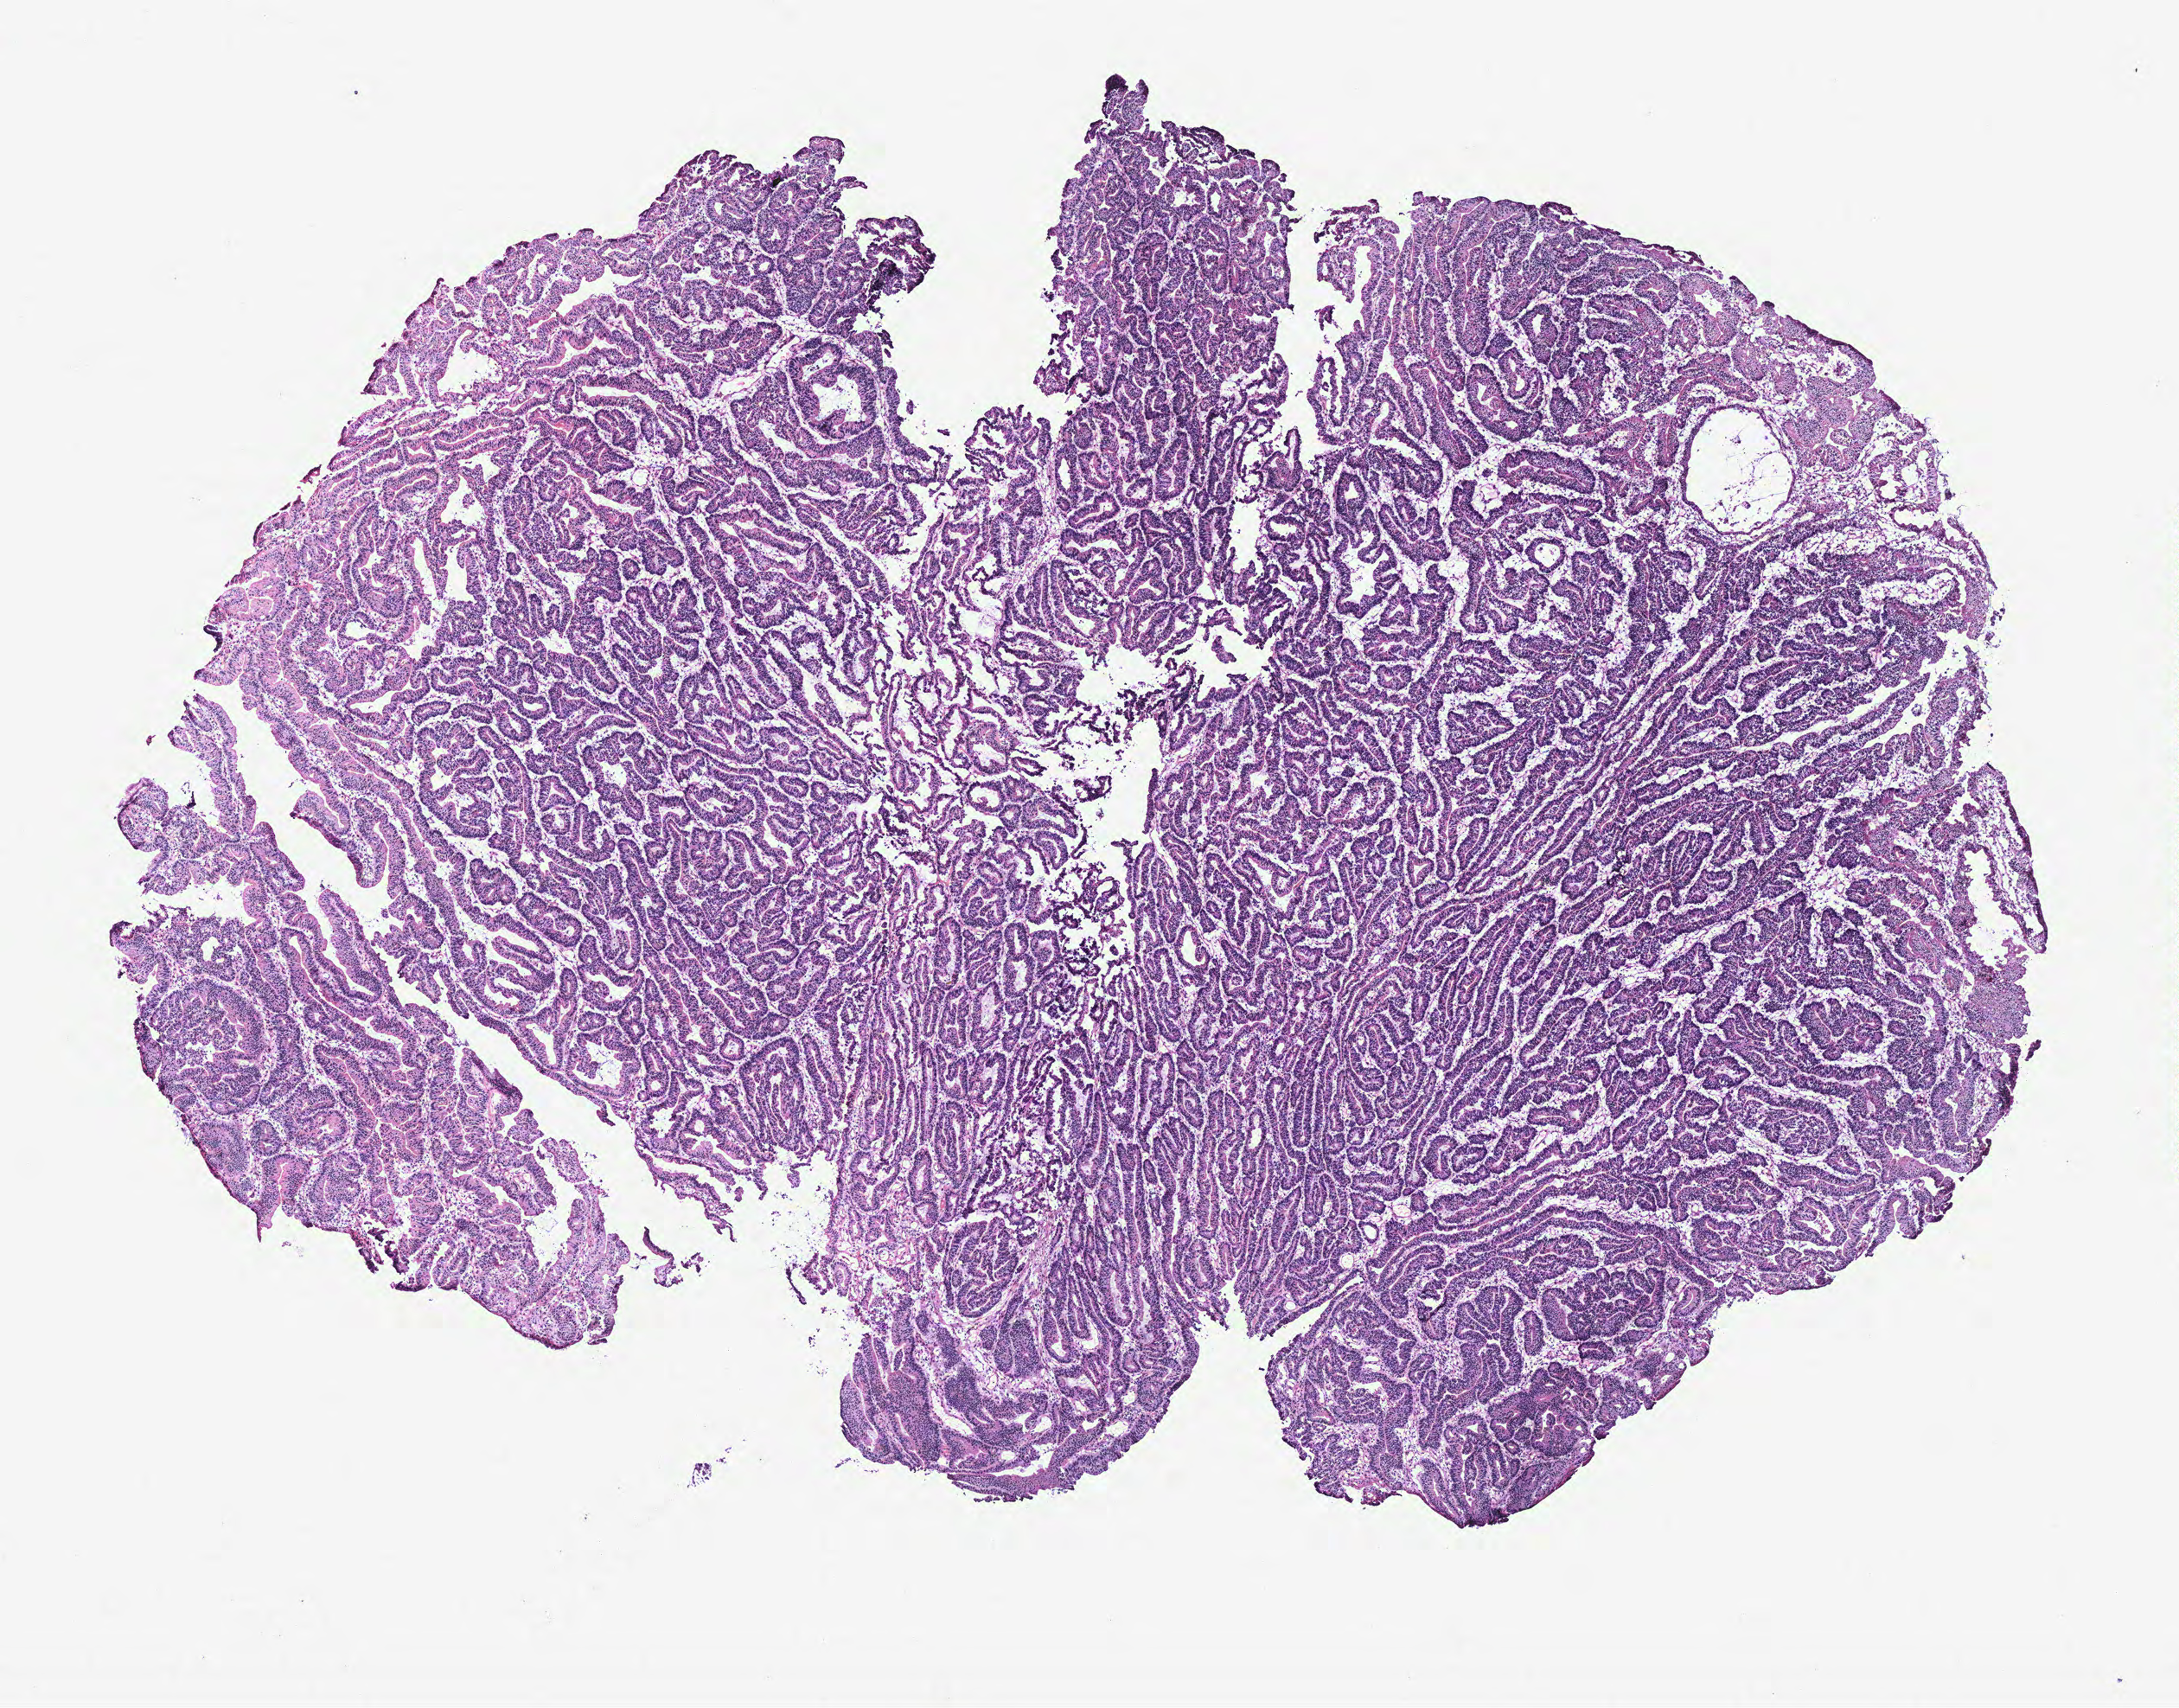
Whole-slide histology image, Hematoxylin and eosin (H&E) stained — a low-resolution overview of the entire scanned area, about 10.1 x 7.9 mm (acquisition: 40x scan), colon, tumour tissue. 73-year-old male patient.
Primary tumour site (as recorded): colon. Histologic diagnosis: Adenocarcinoma, NOS. AJCC pathologic stage: IIB.